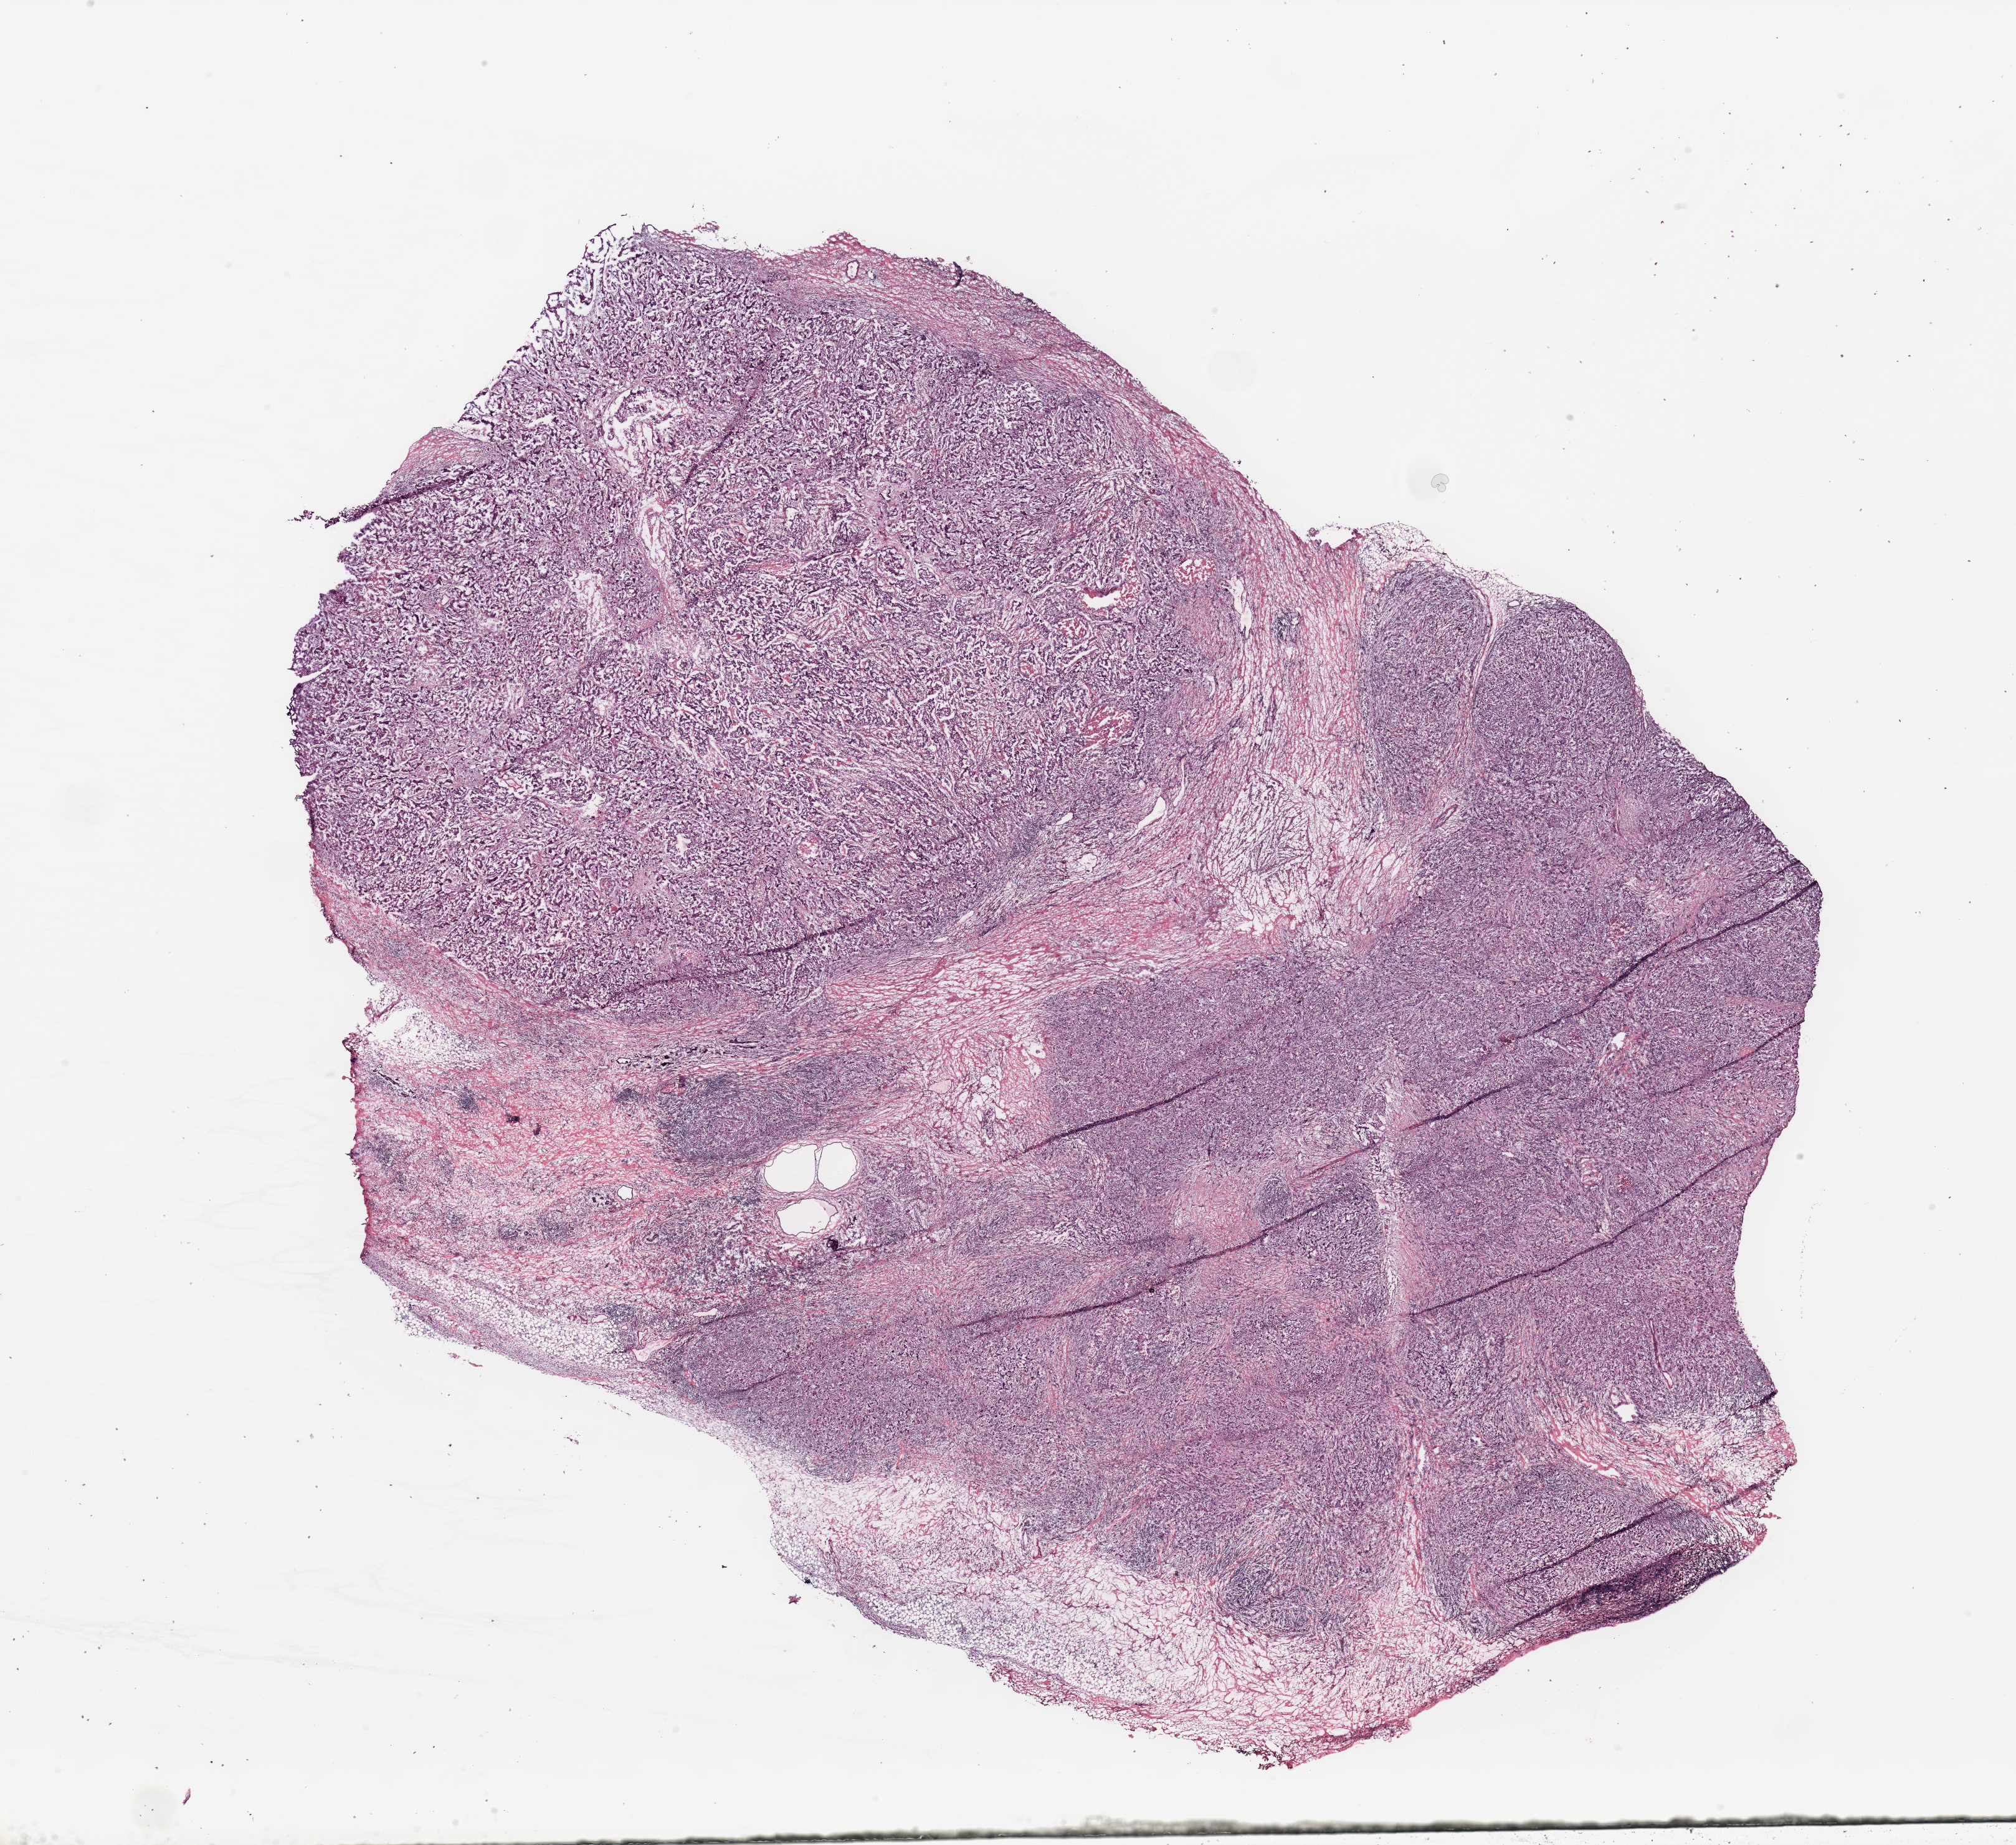
Whole-slide histology image, Hematoxylin and eosin (H&E) stained, a low-resolution overview of the entire scanned area, about 25.6 x 23.4 mm (slide scanned at 20x), tumour tissue sample, breast. Patient: female, age 54 years.
• histologic diagnosis: Infiltrating duct carcinoma, NOS
• AJCC pathologic stage: IIA